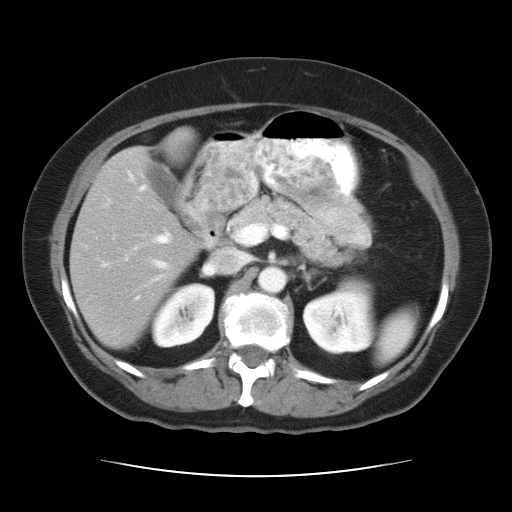
Contrast-enhanced abdominal CT, one axial slice. Slice 17 of 34 in the series (ordered by position). Reconstruction kernel STANDARD. 120 kVp. Intravenous contrast given. Soft-tissue window (W 400 / L 40 HU). 7.5 mm slice thickness. 512 × 512 image matrix. Female patient, age 65 years. From the clinical record (not read from this slice): diagnosis: colorectal cancer liver metastases, imaged before liver resection; multiple liver metastases: yes; largest metastasis: 2.2 cm; disease in both lobes: no.
Annotated regions visible in this slice (manually delineated by an expert):
- hepatic veins: box from (x=138, y=185) to (x=246, y=281) px
- liver: (x=73, y=149)–(x=195, y=347)
- planned liver remnant (the part of the liver to remain after resection): (x=73, y=149)–(x=195, y=347)
- portal vein (with intrahepatic branches): (x=135, y=233)–(x=170, y=249)